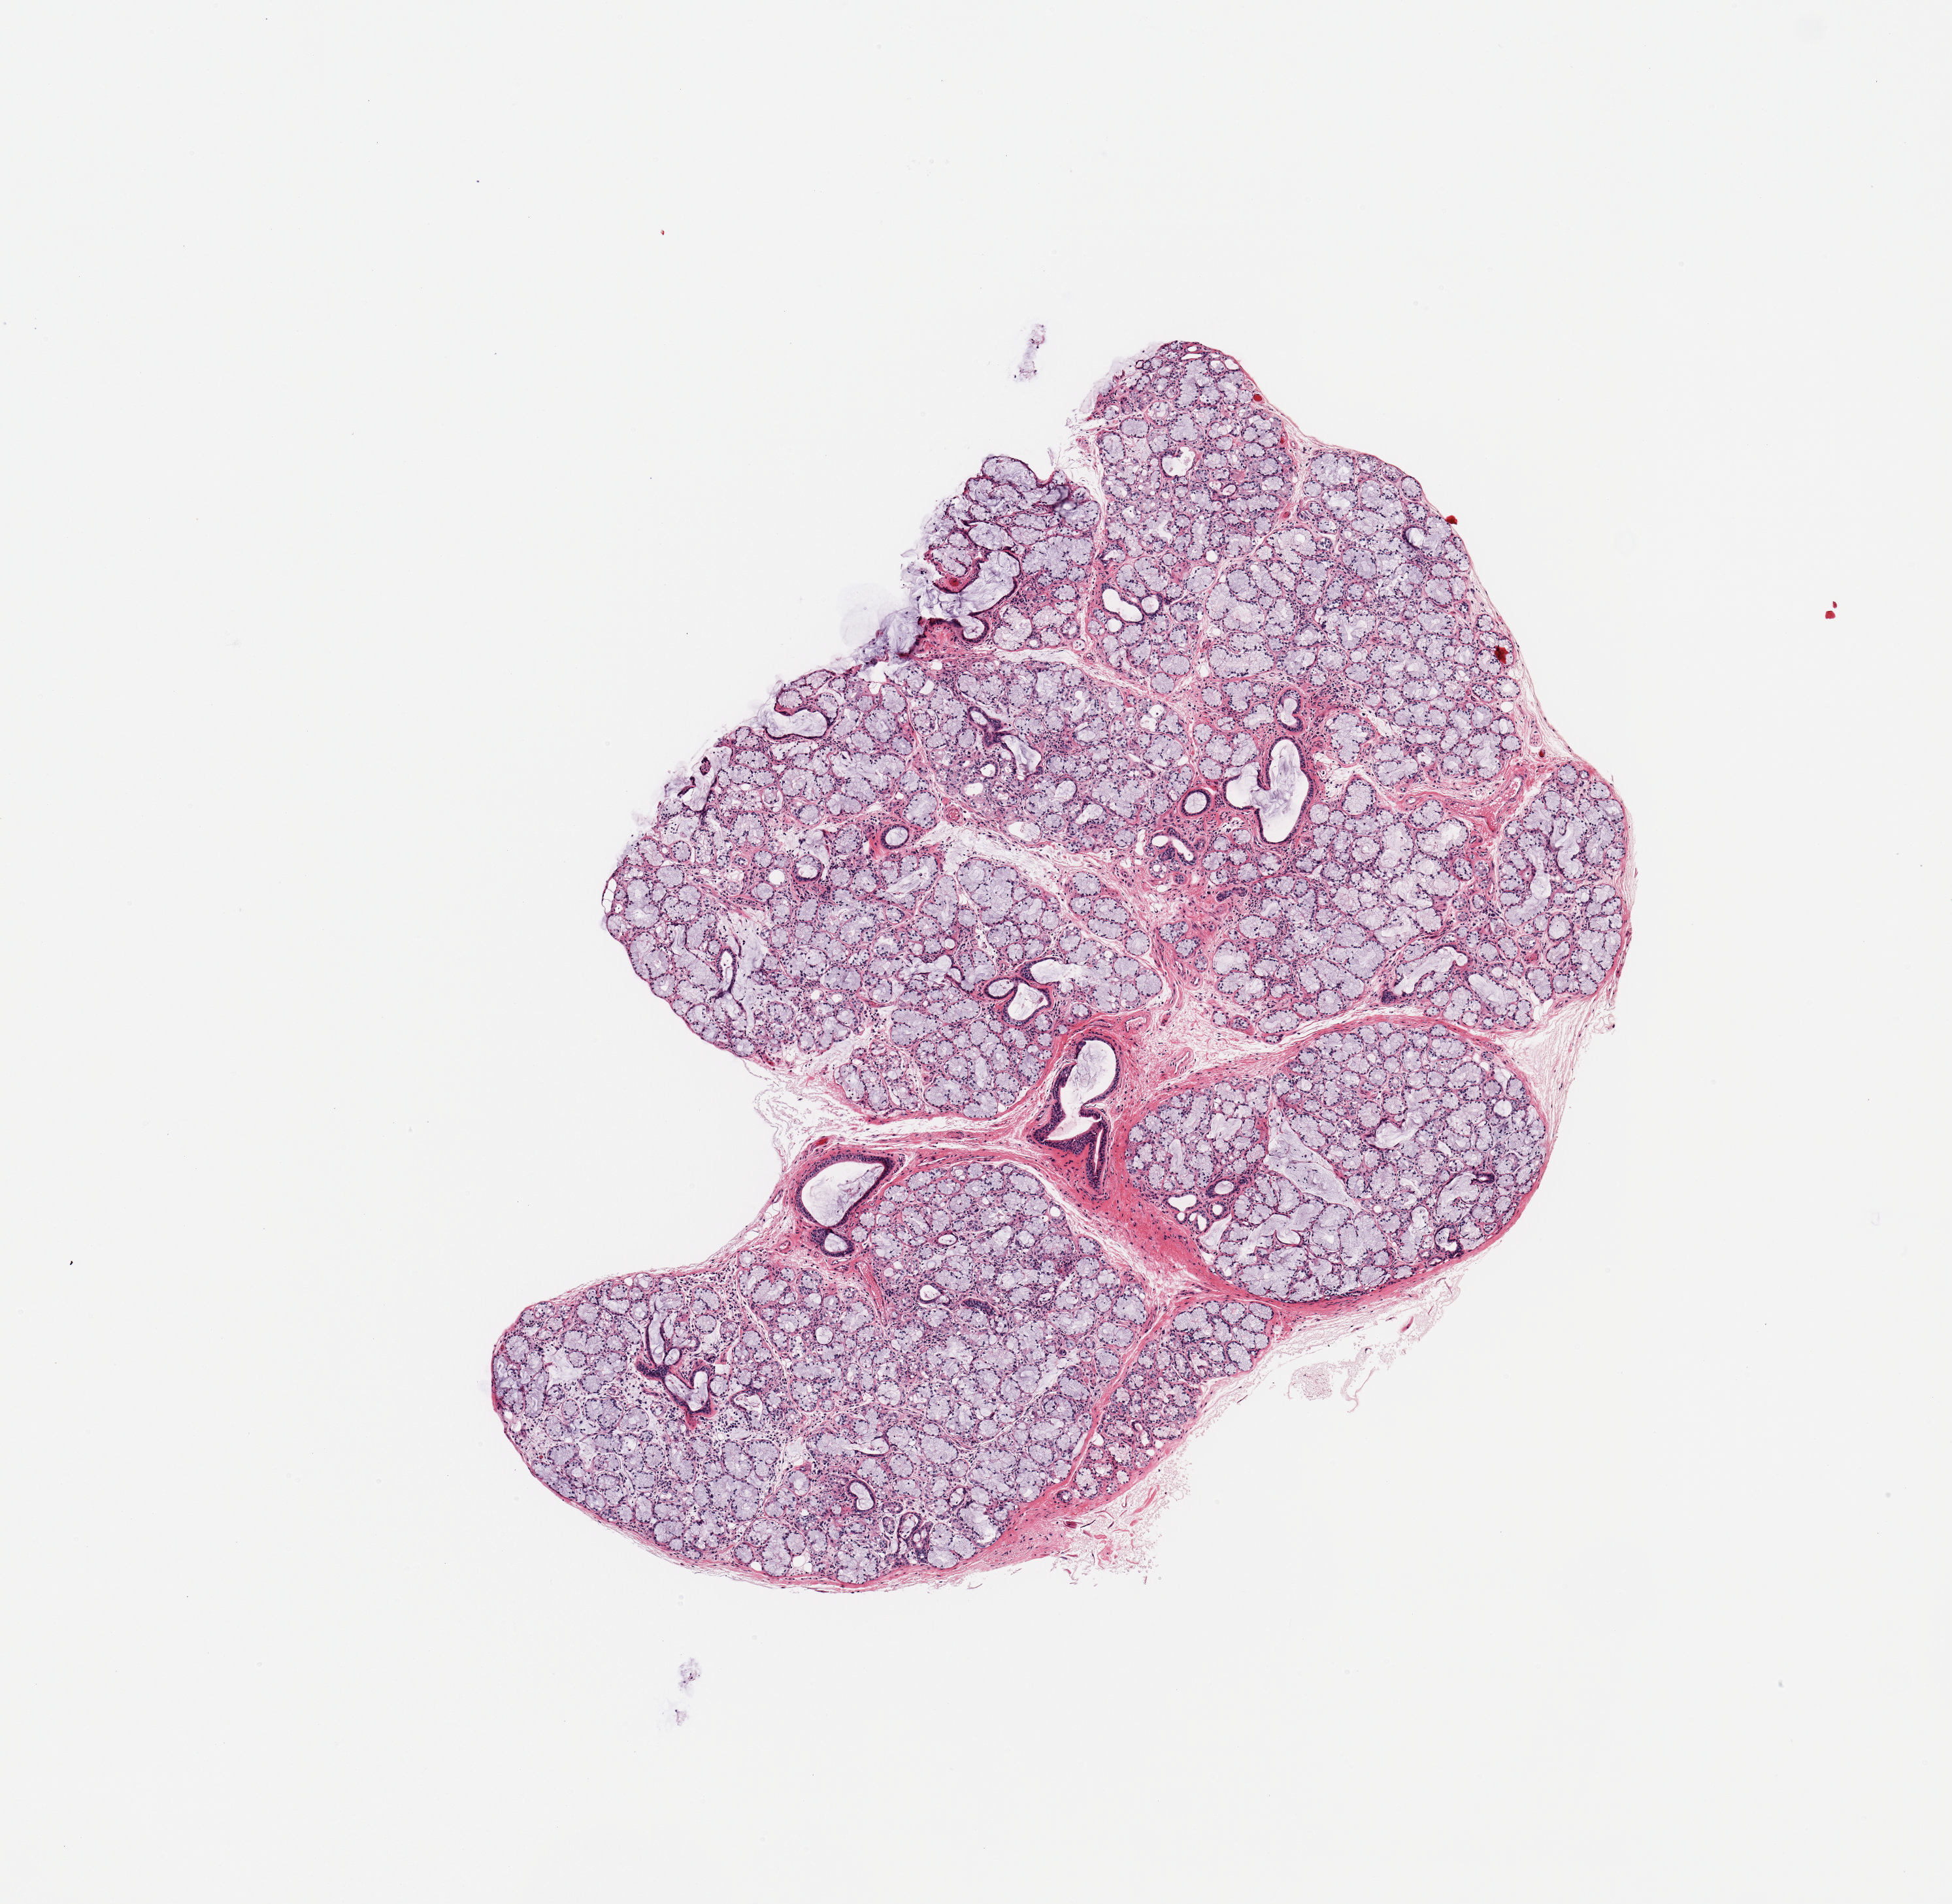
Haematoxylin and eosin whole-slide image, brightfield — whole scanned area (about 5.9 x 5.8 mm) shown as a low-resolution overview. PAXgene-fixed, paraffin-embedded tissue. Section of minor salivary gland (target tissue). Tissue donor sample.
- pathologist's review note for this sample: 1 piece, ~99% glandular parenchyma, good specimen